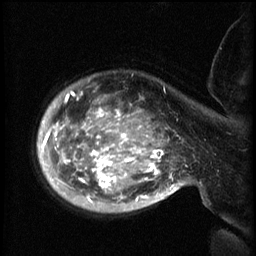
Breast MRI (dynamic contrast-enhanced), one sagittal slice. Position 49 of 60 along the scan axis. 3 images stored at this slice position (order not interpretable as contrast timing). 1.5 T. TE 4.2 ms, TR 8.2 ms. 2.3 mm slice thickness. 256 × 256 image matrix, field of view 200 × 200 mm. Patient: female, 50 years.
Annotated regions visible in this slice (semi-automatically segmented with operator editing):
- analysis volume of interest (the breast-tissue region the enhancement analysis was run in; not a lesion): bounding box (x1, y1, x2, y2) in pixels: (50, 80, 169, 213)
- tumour enhancement mask (voxels above the 70 % enhancement threshold inside the analysis volume of interest): (50, 92, 165, 203)